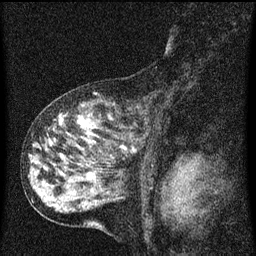
Breast MRI (dynamic contrast-enhanced), one sagittal slice; position 32 of 60 along the scan axis; dynamic contrast-enhanced series, image 2 of 3 at this slice position (ordered by acquisition); 1.5 T; TE 4.2 ms, TR 8 ms; 2 mm slice thickness; 256 × 256 image matrix, field of view 180 × 180 mm. Patient: female, 55 years.
Outlined on this slice (semi-automatically segmented with operator editing):
- analysis volume of interest (the breast-tissue region the enhancement analysis was run in; not a lesion): bounding box [x1, y1, x2, y2] px = [38, 92, 151, 159]
- tumour enhancement mask (voxels above the 70 % enhancement threshold inside the analysis volume of interest): [60, 116, 135, 151]